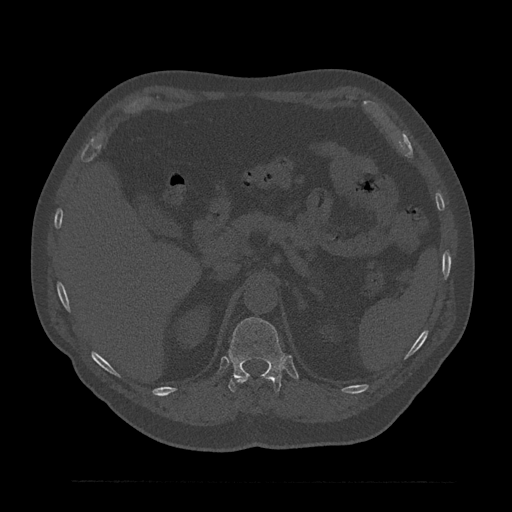
CT including the spine, one axial slice. Slice 249 of 797 in the series (ordered by position). Reconstruction kernel Br40s/3. 120 kVp. Bone window (W 1800 / L 400 HU). 0.5 mm slice thickness. 512 × 512 image matrix. Patient: male, 61 years. Case-level facts recorded for this patient, not image findings: primary cancer: prostate.
Outlined on this slice (semi-automatic segmentation, software-assisted and operator-edited):
- T11 vertebra: bounding box <237,378,272,384> (left, top, right, bottom; pixels)
- T12 vertebra: <228,317,285,392>